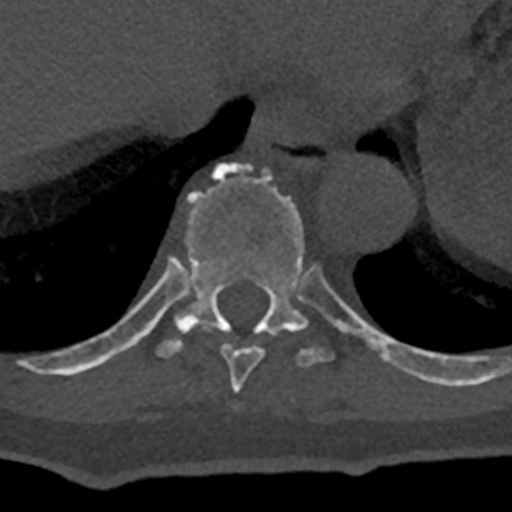
CT including the spine, one axial slice; slice 622 of 797 in the series (ordered by position); reconstruction kernel Br40s/3; bone window (W 1800 / L 400 HU); 0.5 mm slice thickness; 512 × 512 image matrix, field of view 160 × 160 mm. Male patient, age 74 years. Case-level facts recorded for this patient, not image findings: primary cancer: renal; vertebrae with lytic lesions (as recorded): T10, L1, L2, L3, L4, L5.
Annotated regions visible in this slice (semi-automatic segmentation, software-assisted and operator-edited):
- T10 vertebra: bounding box <70,162,432,383> (left, top, right, bottom; pixels)
- T9 vertebra: <181,324,277,393>